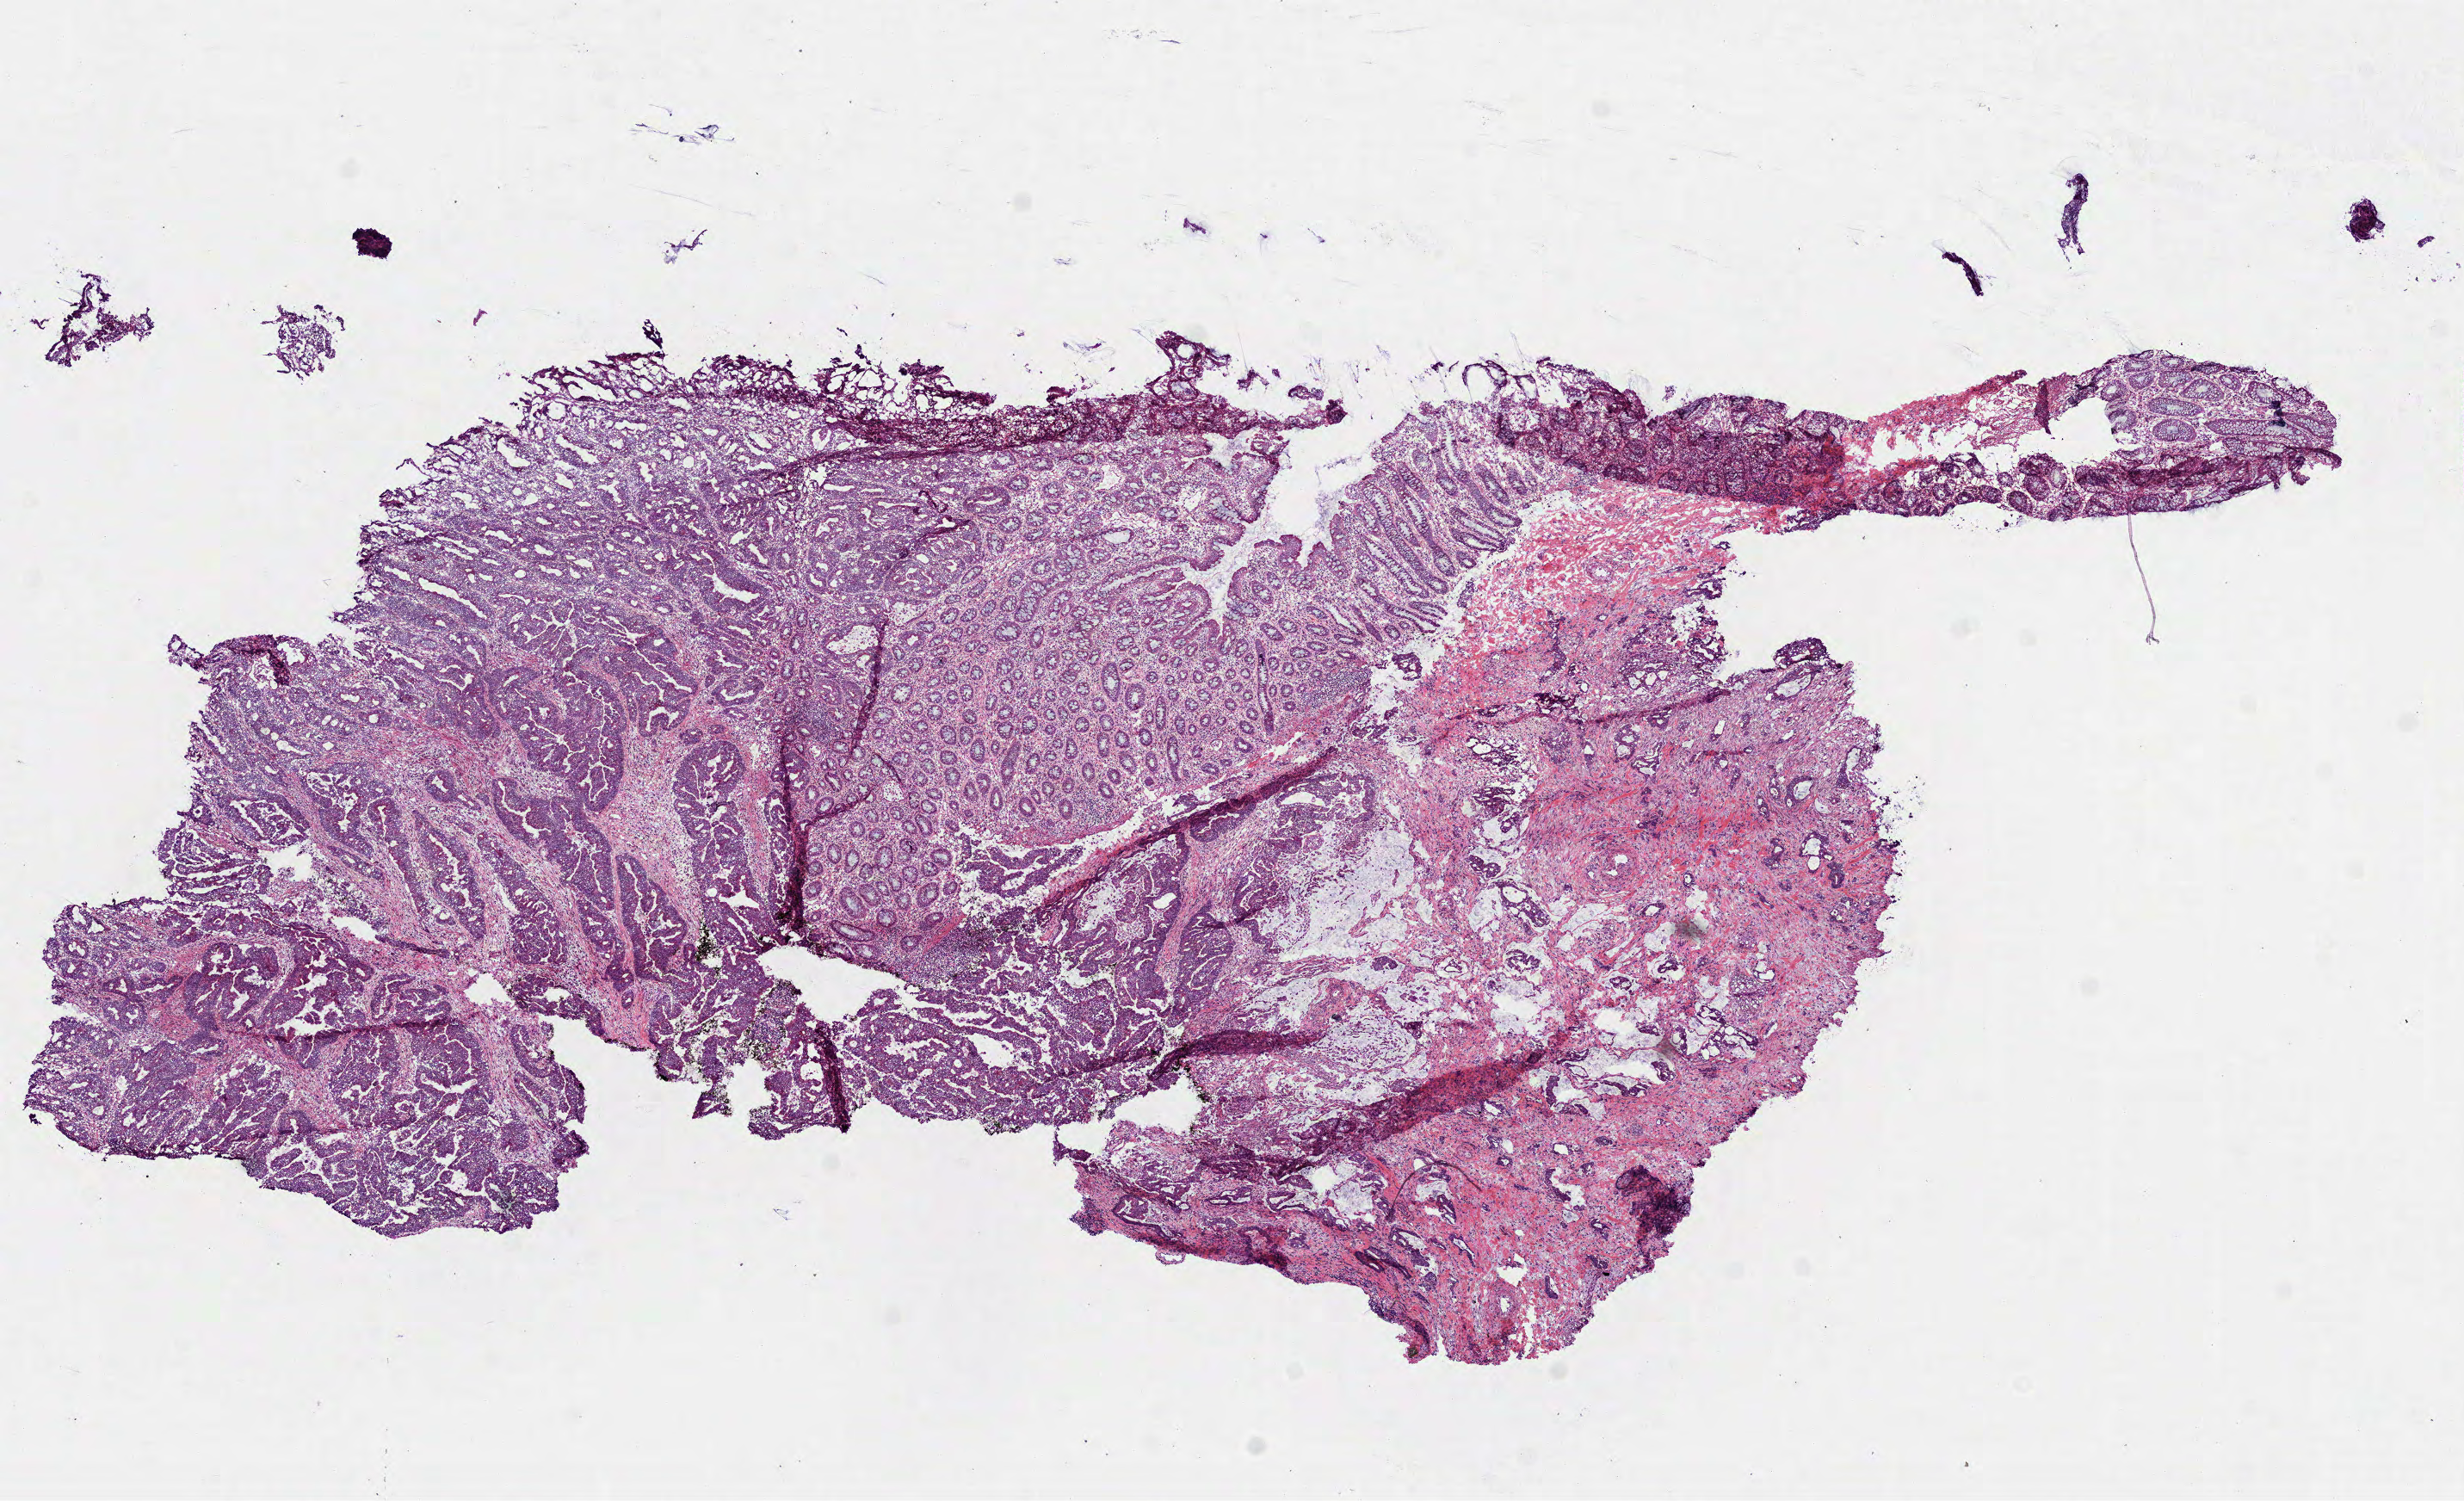
Digitized Hematoxylin and eosin (H&E) stained tissue section (whole slide) — low-resolution overview of the scanned area, about 11.5 x 7.0 mm (from a 40x scan). Frozen section from the bottom of the tissue portion. Sample: primary tumour, rectum. Female patient; age at initial diagnosis 72 years. Slide review estimates, as recorded: tumour cells 78%, tumour nuclei 75%.
Diagnosis: Adenocarcinoma, NOS (rectosigmoid junction).